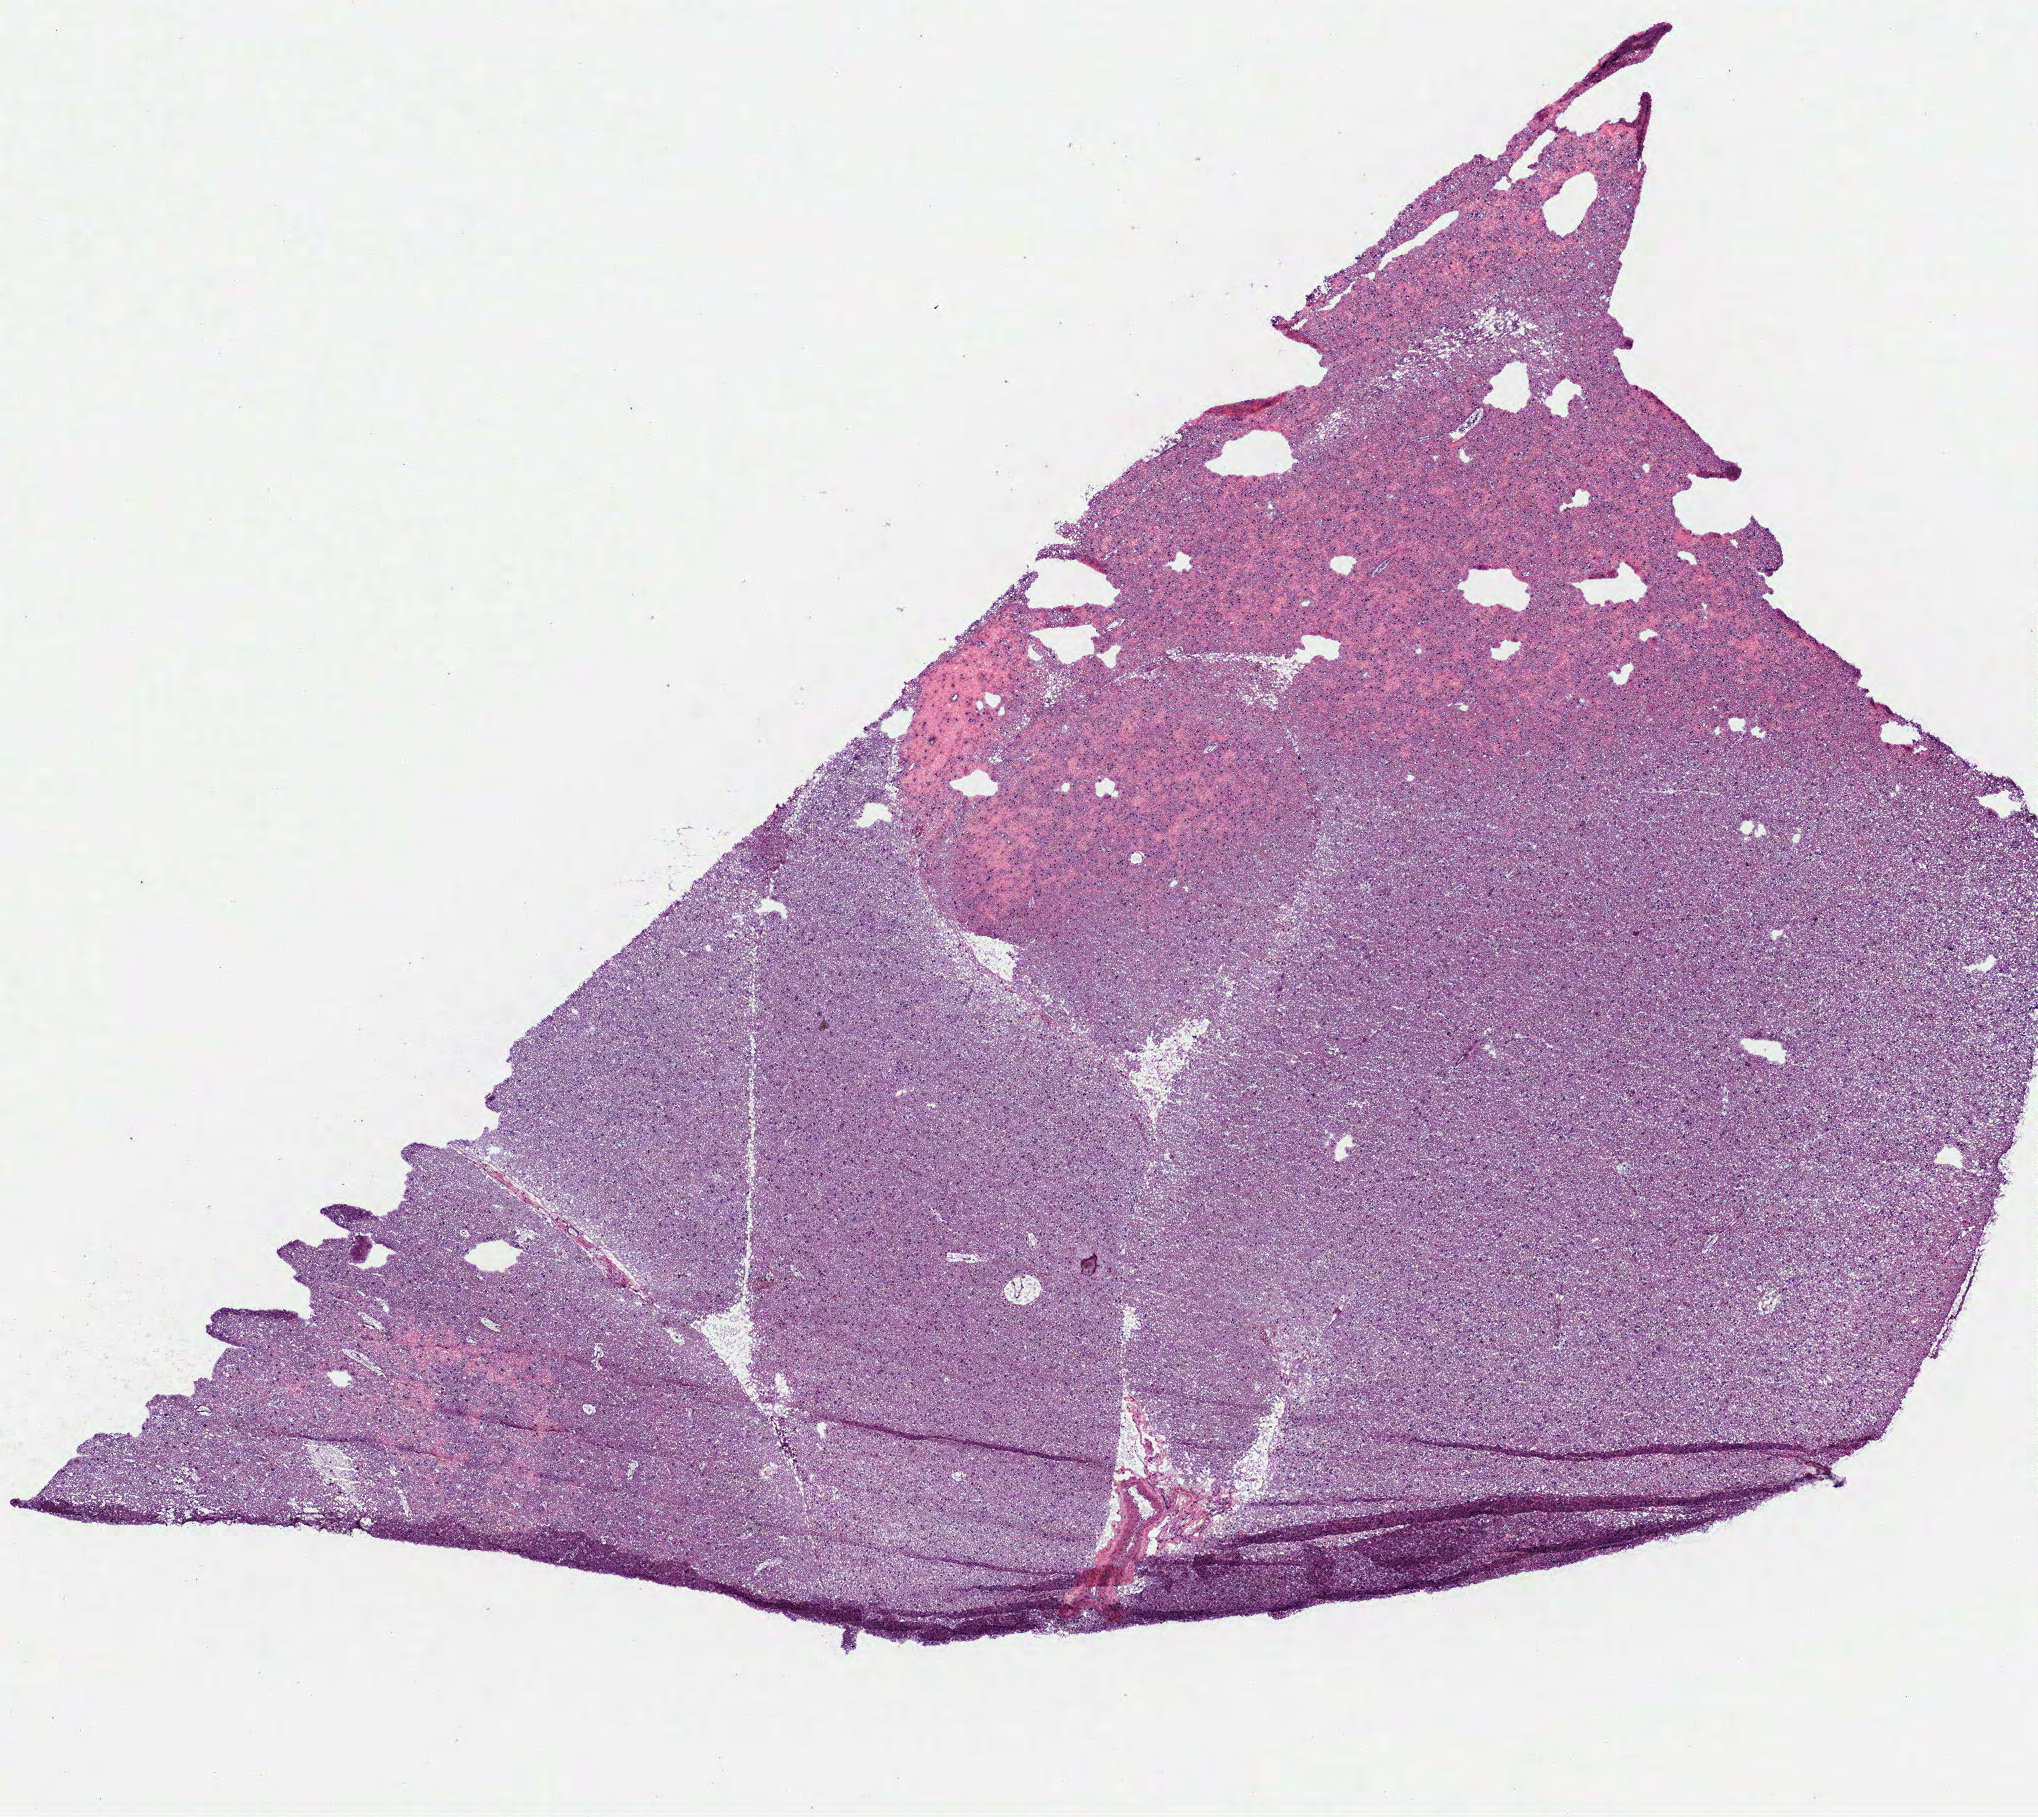
Digitized H&E tissue section (whole slide), low-resolution overview of the scanned area, about 8.2 x 7.3 mm (slide scanned at 40x); frozen section from the top of the tissue portion; brain, primary tumour sample. Female patient; age at initial diagnosis 41 years. Histologic grade: G3 (poorly differentiated). Slide review estimates, as recorded: tumour cells 90%, tumour nuclei 60%, normal cells 10%, stromal cells 0%, necrosis 0%.
Histologic diagnosis: Oligodendroglioma, anaplastic.